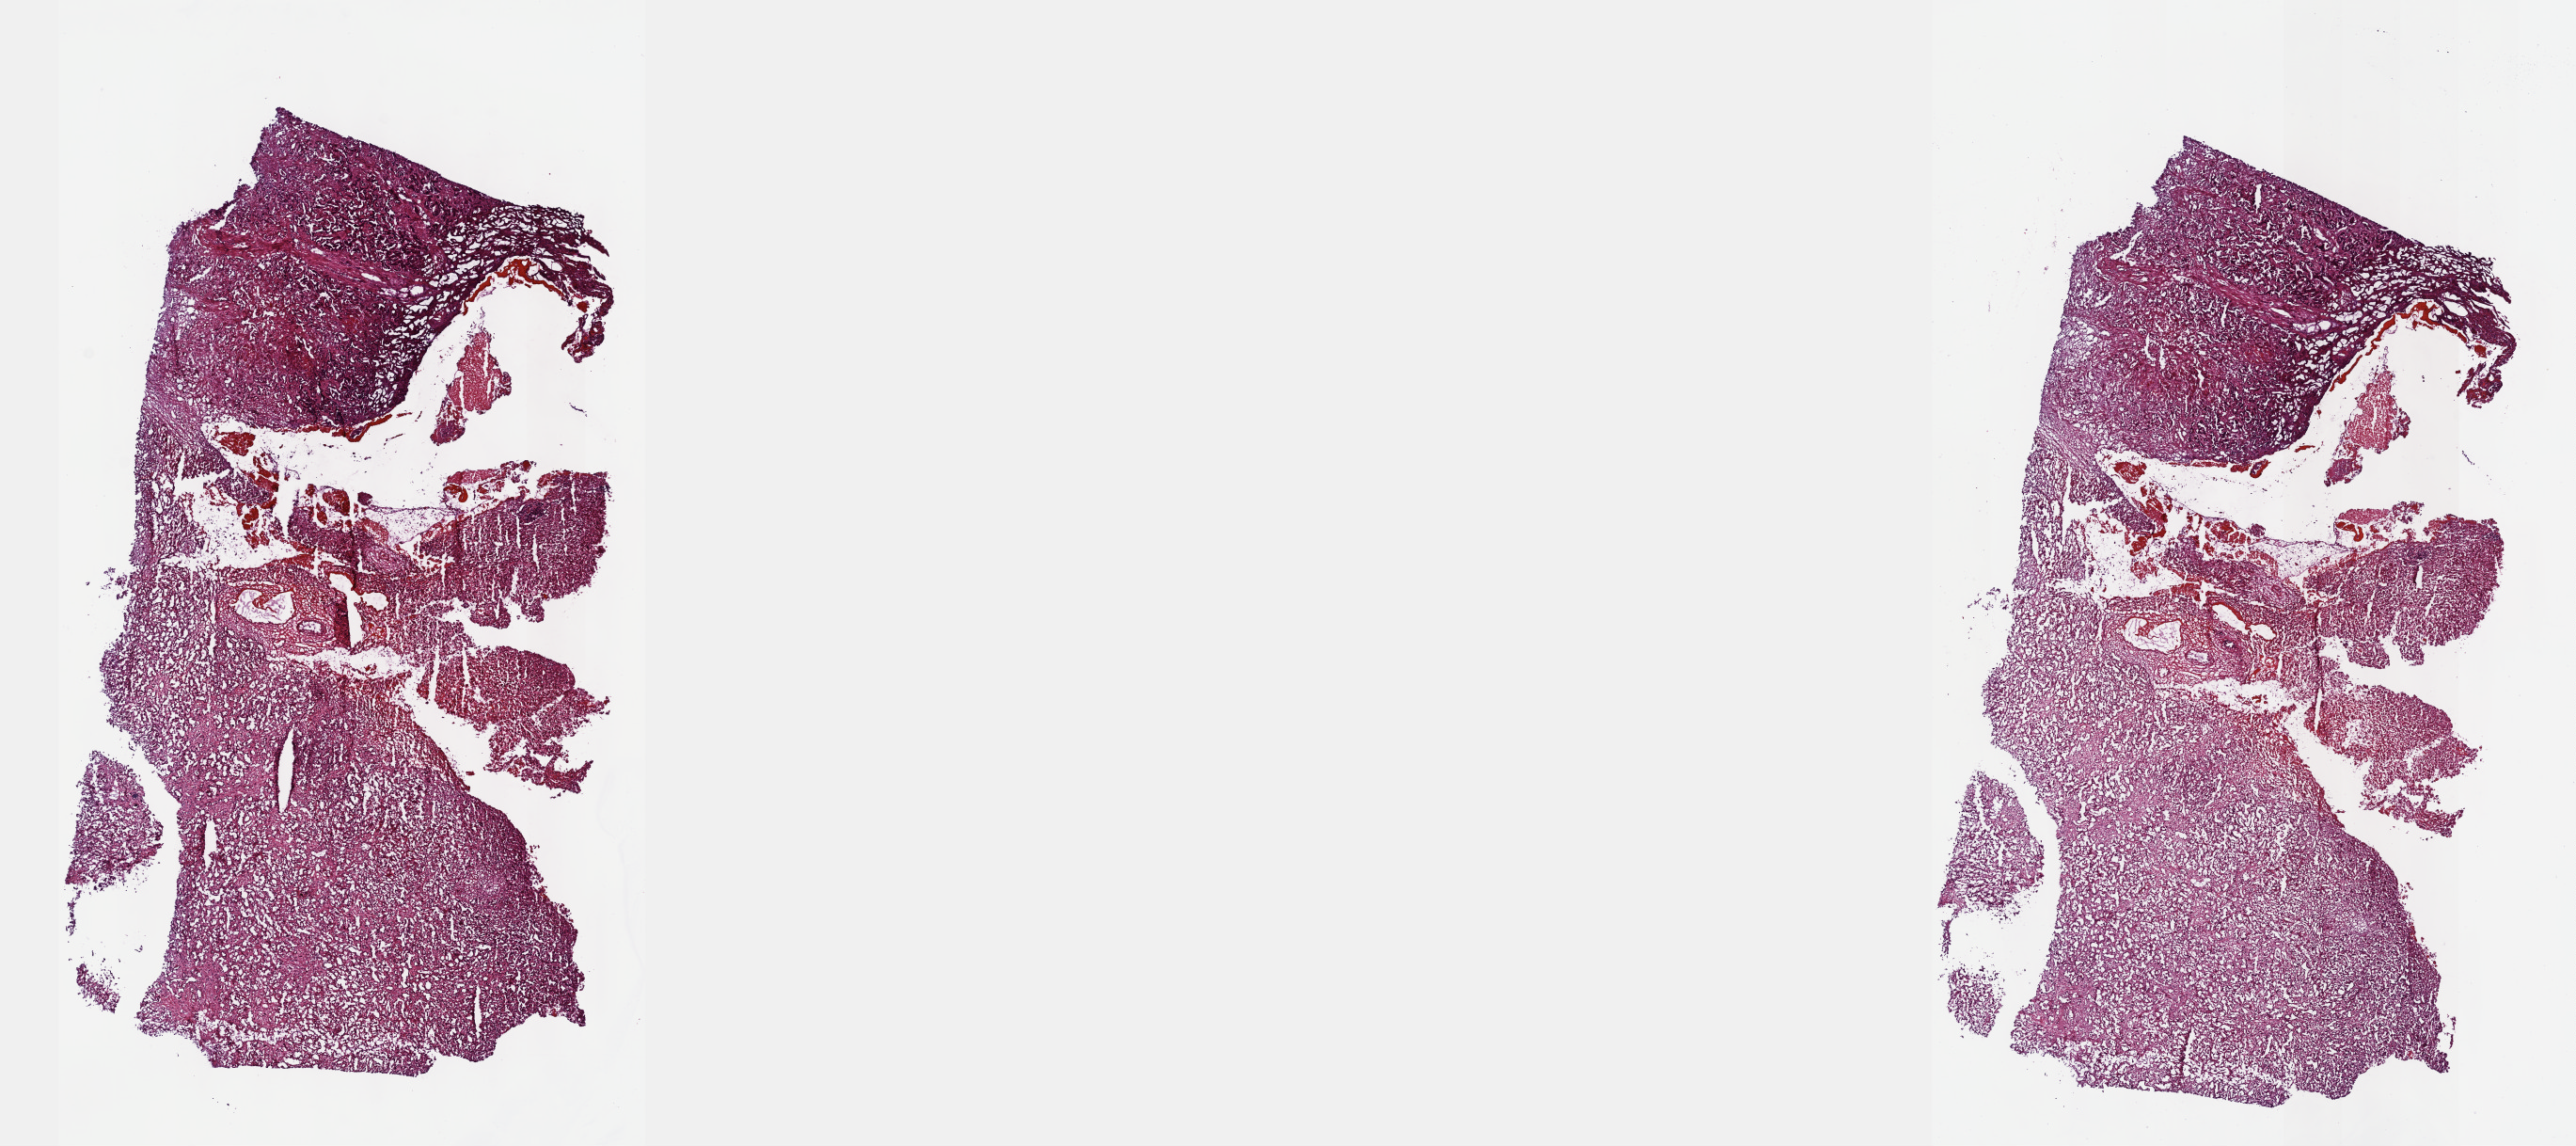
Hematoxylin and eosin (H&E) stained whole-slide image, whole scanned area (about 22.1 x 9.8 mm, from a 40x scan) shown as a low-resolution overview. Frozen section. Sample: primary tumour, bile duct. Female patient; age at initial diagnosis 62 years. Histologic grade: G2 (moderately differentiated). Composition of this section per pathologist review: tumour cells 100%, tumour nuclei 65%, normal cells 0%, stromal cells 0%, necrosis 0%. Infiltration values recorded for this section: lymphocyte infiltration 2%, monocyte infiltration 0%, neutrophil infiltration 0%.
* AJCC pathologic stage: III (7th edition)
* histologic diagnosis: Cholangiocarcinoma (intrahepatic bile duct)